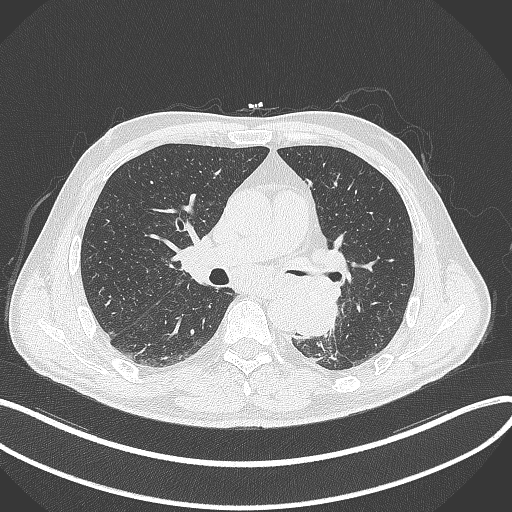
Chest CT, one axial slice; slice 193 of 329 in the series (ordered by position); 120 kVp; lung window (W 1500 / L -600 HU); 1 mm slice thickness; 512 × 512 image matrix, field of view 400 × 400 mm. Male patient, age 59 years. From the clinical record (not read from this slice): clinical TNM (as recorded): T2a N2 M0.
Structures marked on this image (bounding box drawn by a radiologist):
- lung tumour (recorded histology: squamous cell carcinoma): box from (x=290, y=278) to (x=343, y=340) px